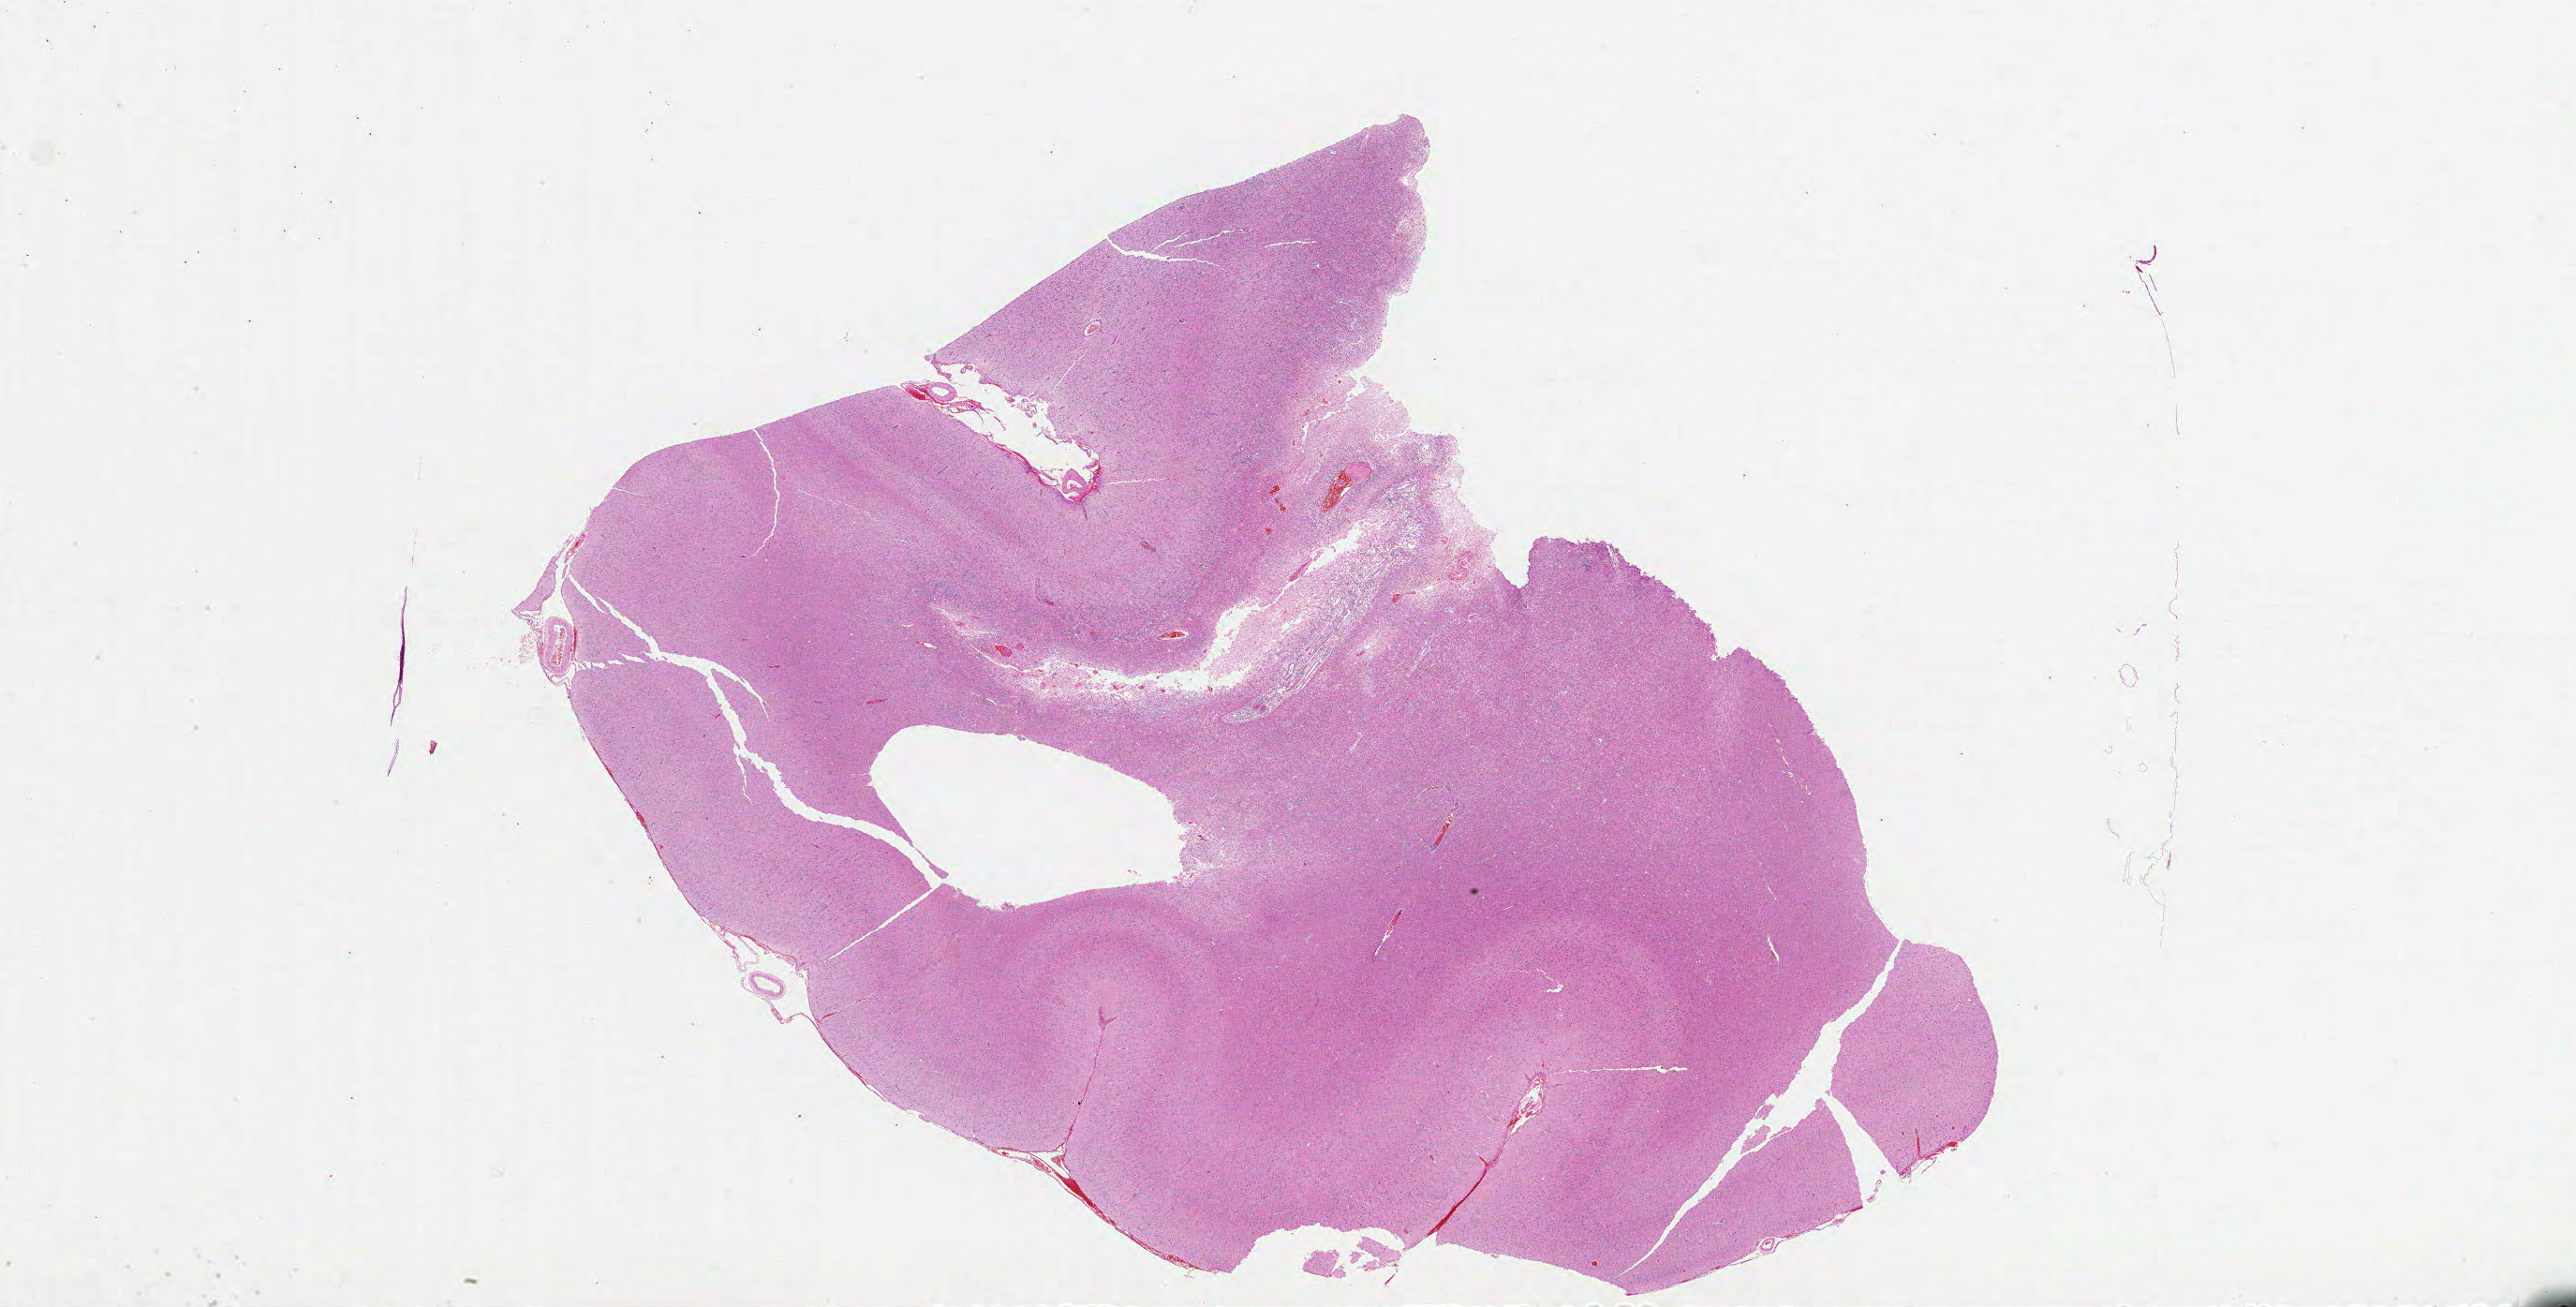
Digitized H&E tissue section (whole slide) — whole scanned area (about 44.0 x 22.3 mm, slide scanned at 20x) shown as a low-resolution overview. Formalin-fixed paraffin-embedded (FFPE) diagnostic section. Brain, primary tumour sample. Patient: male, age at initial diagnosis 61 years.
Histologic diagnosis: Glioblastoma.